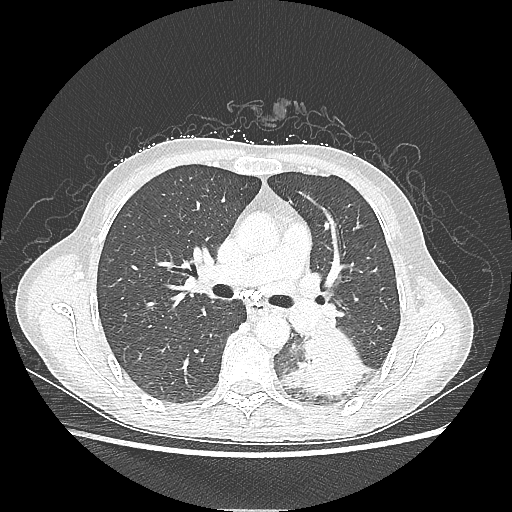
Chest CT, one axial slice; lung window (W 1500 / L -600 HU); 512 × 512 image matrix. Patient: female, 53 years. Case-level facts recorded for this patient, not image findings: clinical TNM (as recorded): T3 N0 M0.
Outlined on this slice (bounding box drawn by a radiologist):
- lung tumour (recorded histology: adenocarcinoma): bounding box (x1, y1, x2, y2) in pixels: (280, 333, 373, 400)